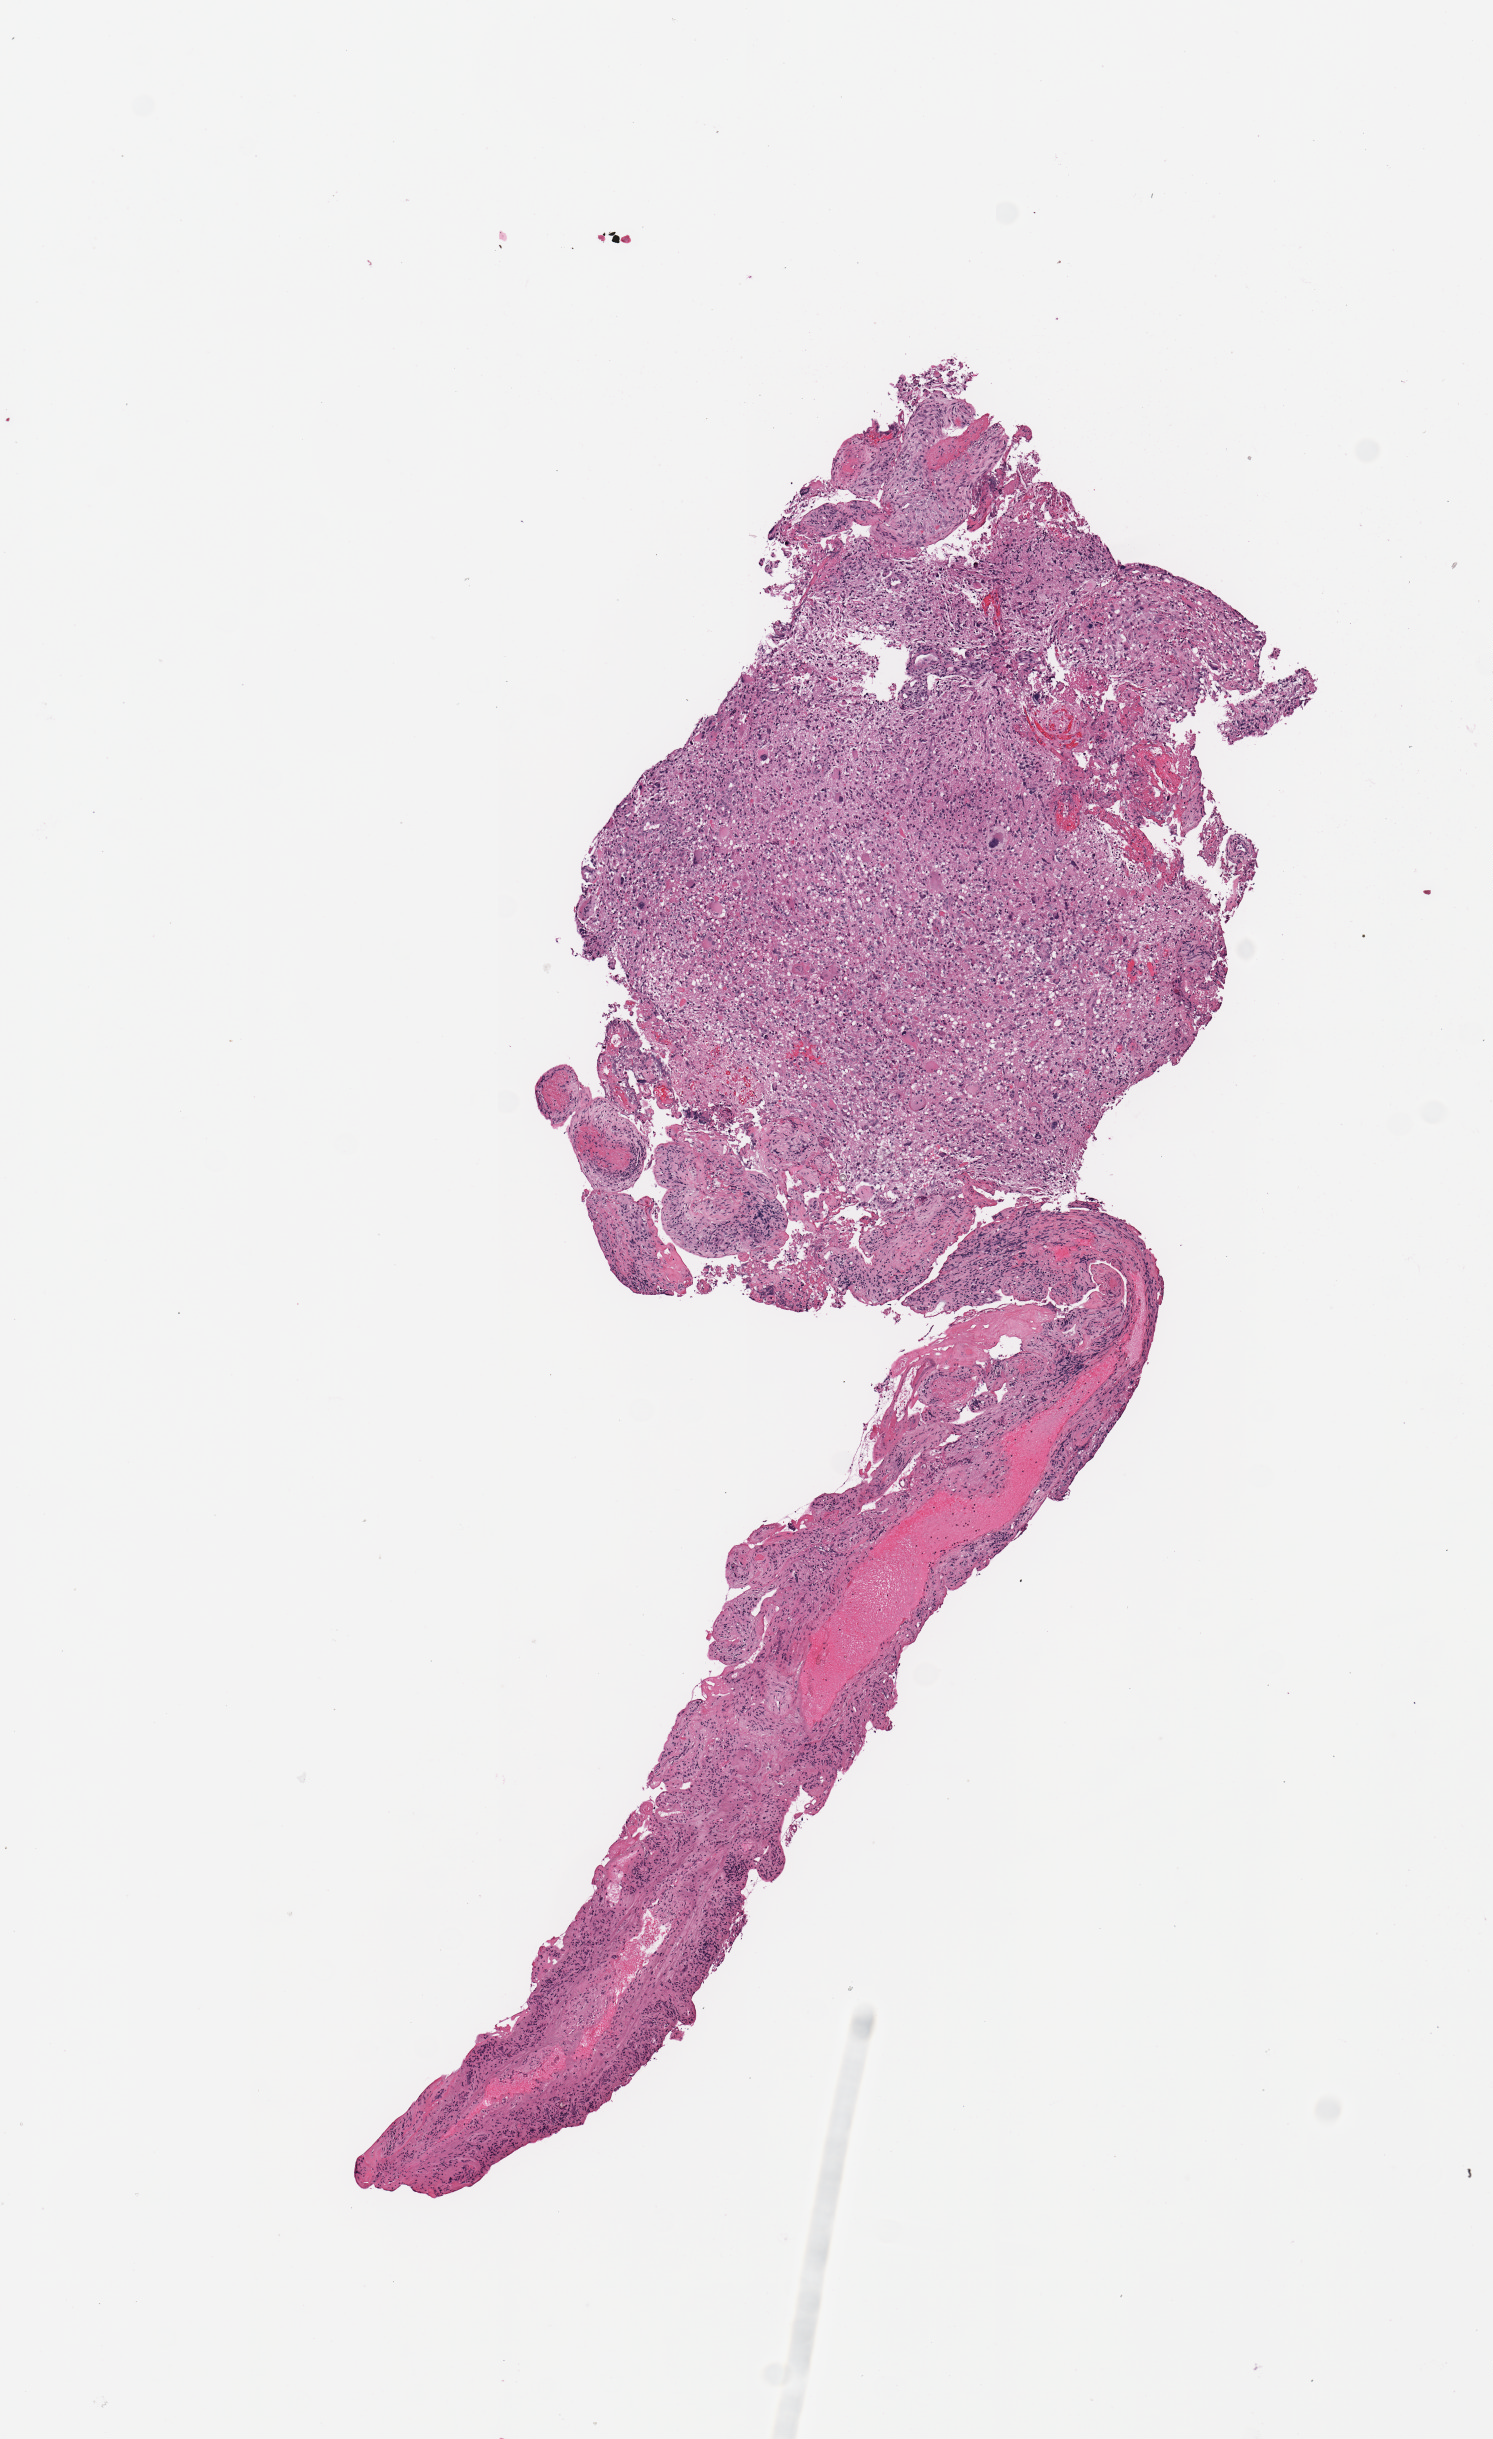
Digitized H&E tissue section (whole slide) — whole scanned area (about 5.9 x 9.6 mm, from a 20x scan) shown as a low-resolution overview. Tumour tissue sample, sampled site: brain. 38-year-old female patient. Pathologist review of this section (percent, as recorded): tumour nuclei 70%, necrosis 5%.
- diagnosis: Glioblastoma
- primary tumour site (as recorded): temporal lobe